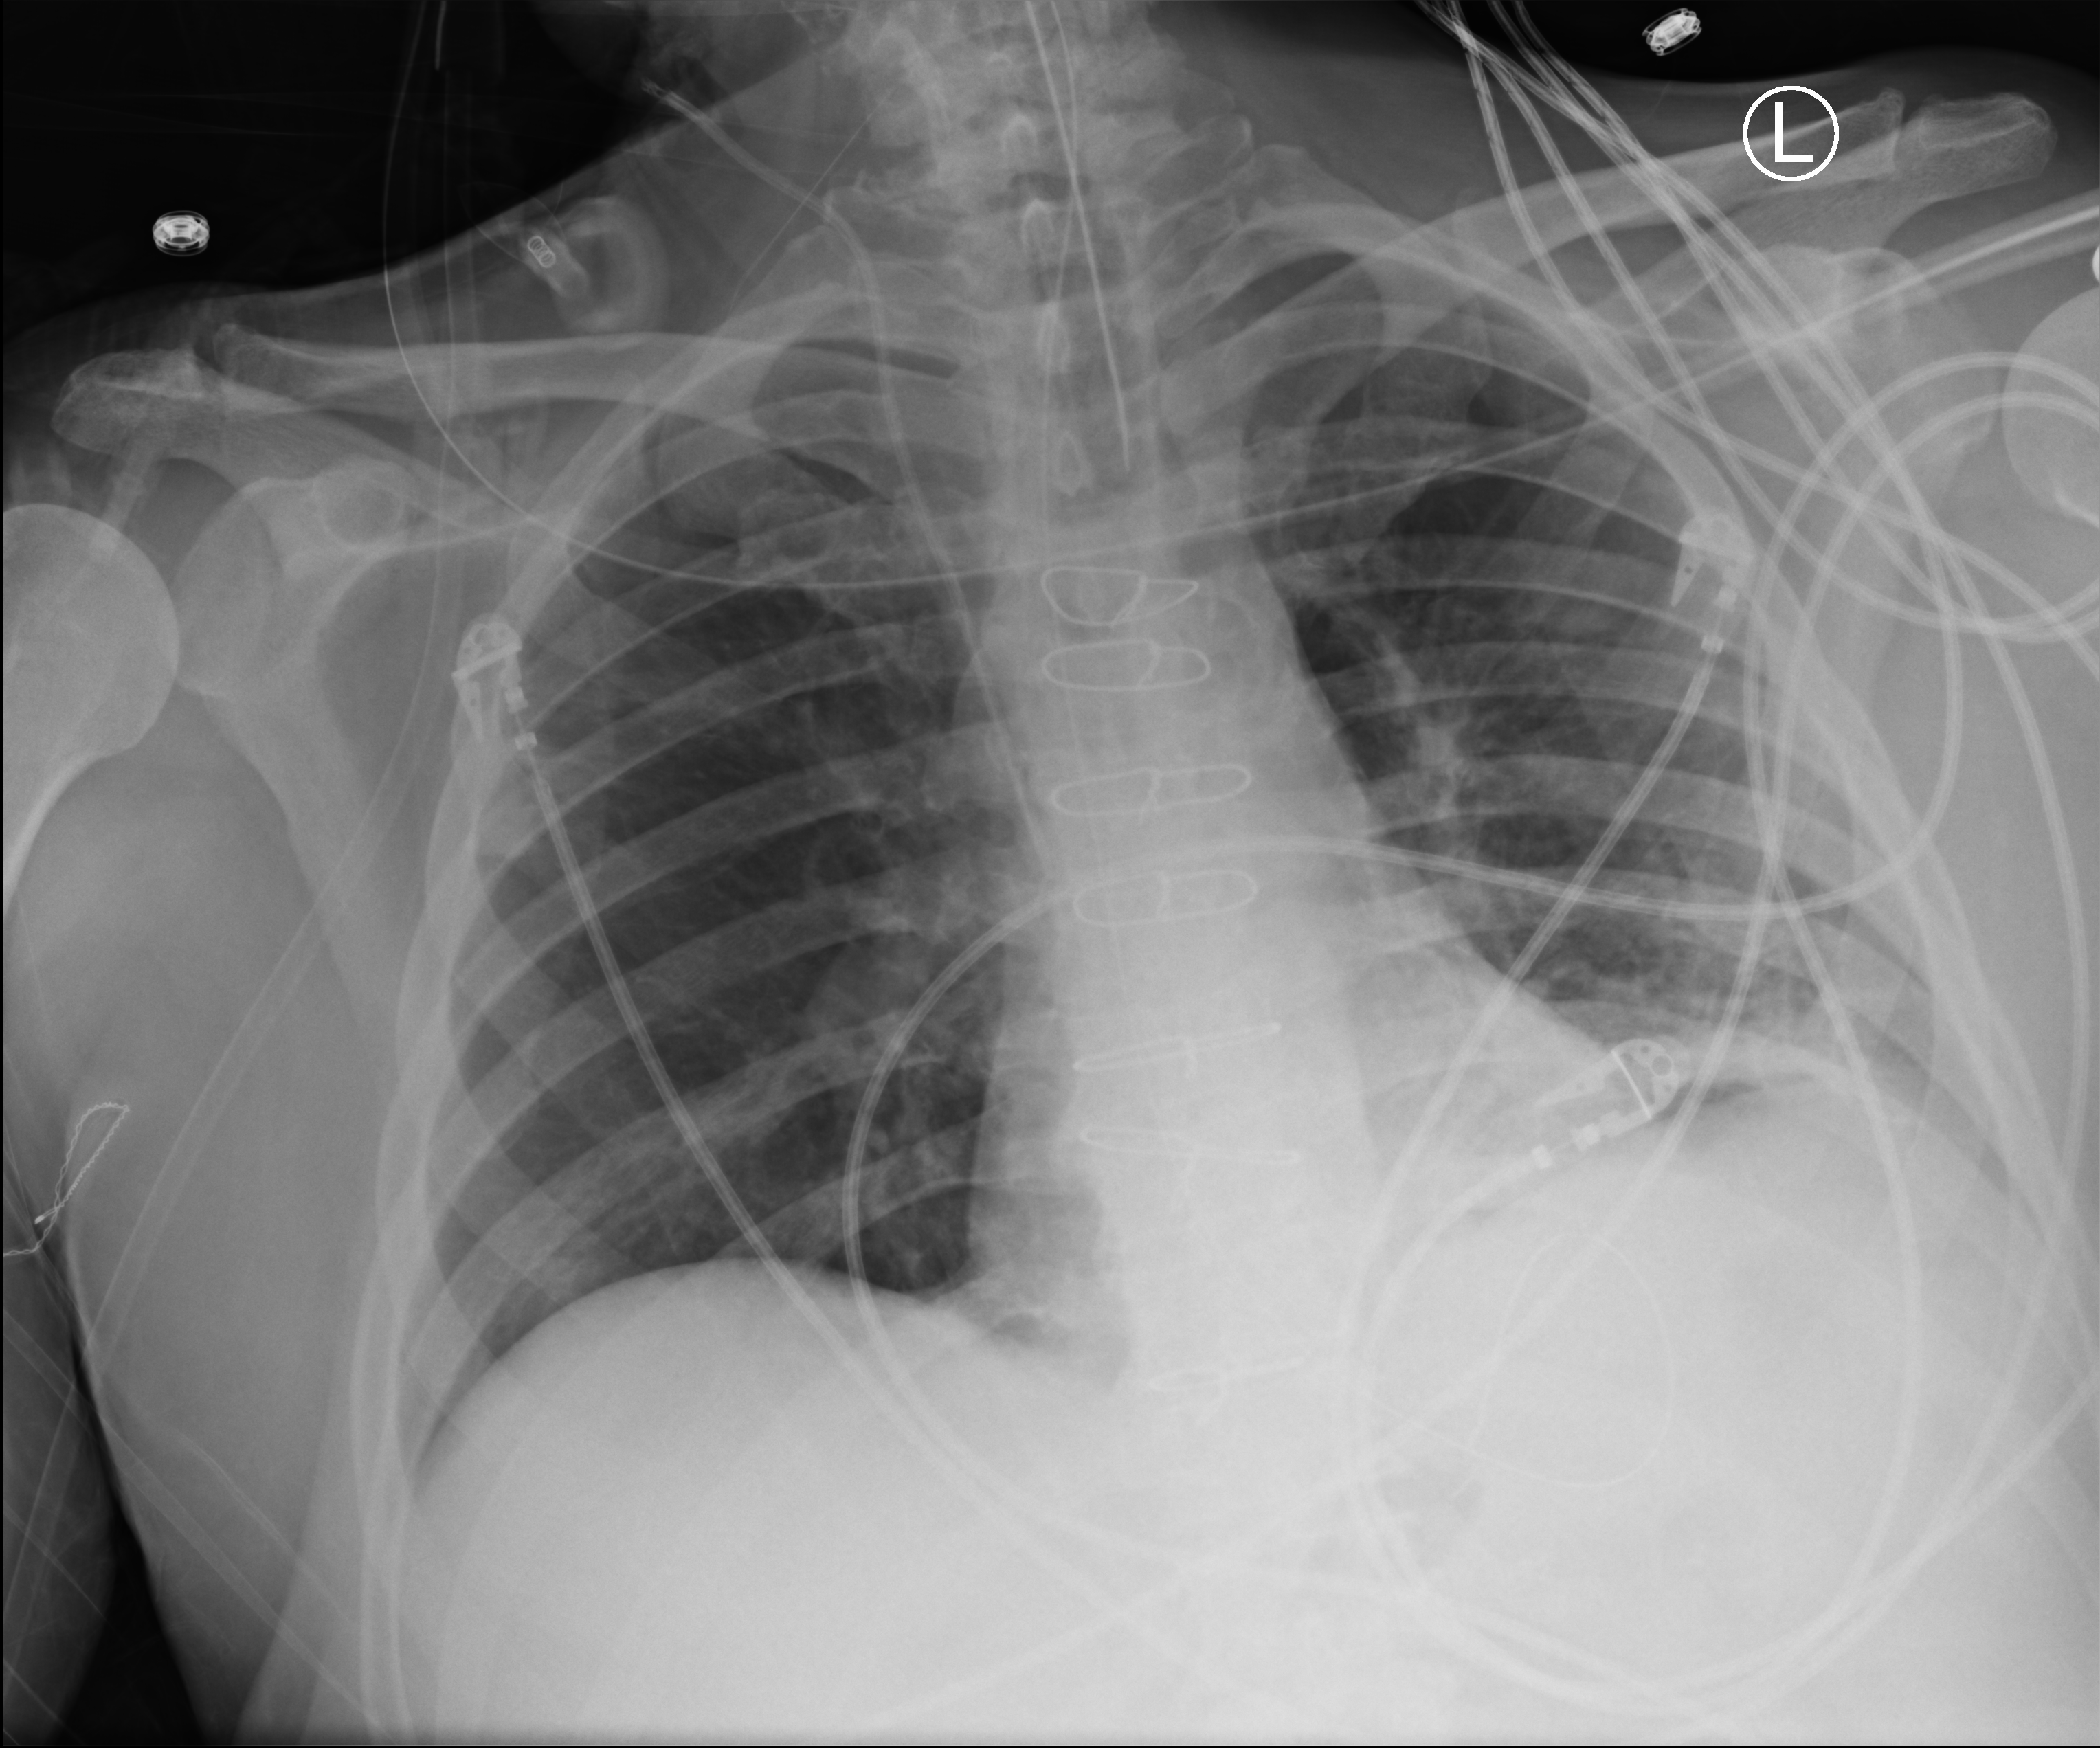
Portable chest radiograph; anteroposterior (AP) projection. Patient hospitalised with COVID-19; male, aged 60–74 years.
From the hospital-stay record, not from the radiograph (when in the stay this image was taken is not recorded): mechanically ventilated during this hospital stay: yes; other chronic lung disease (admission record): no; chronic kidney disease (admission record): no.